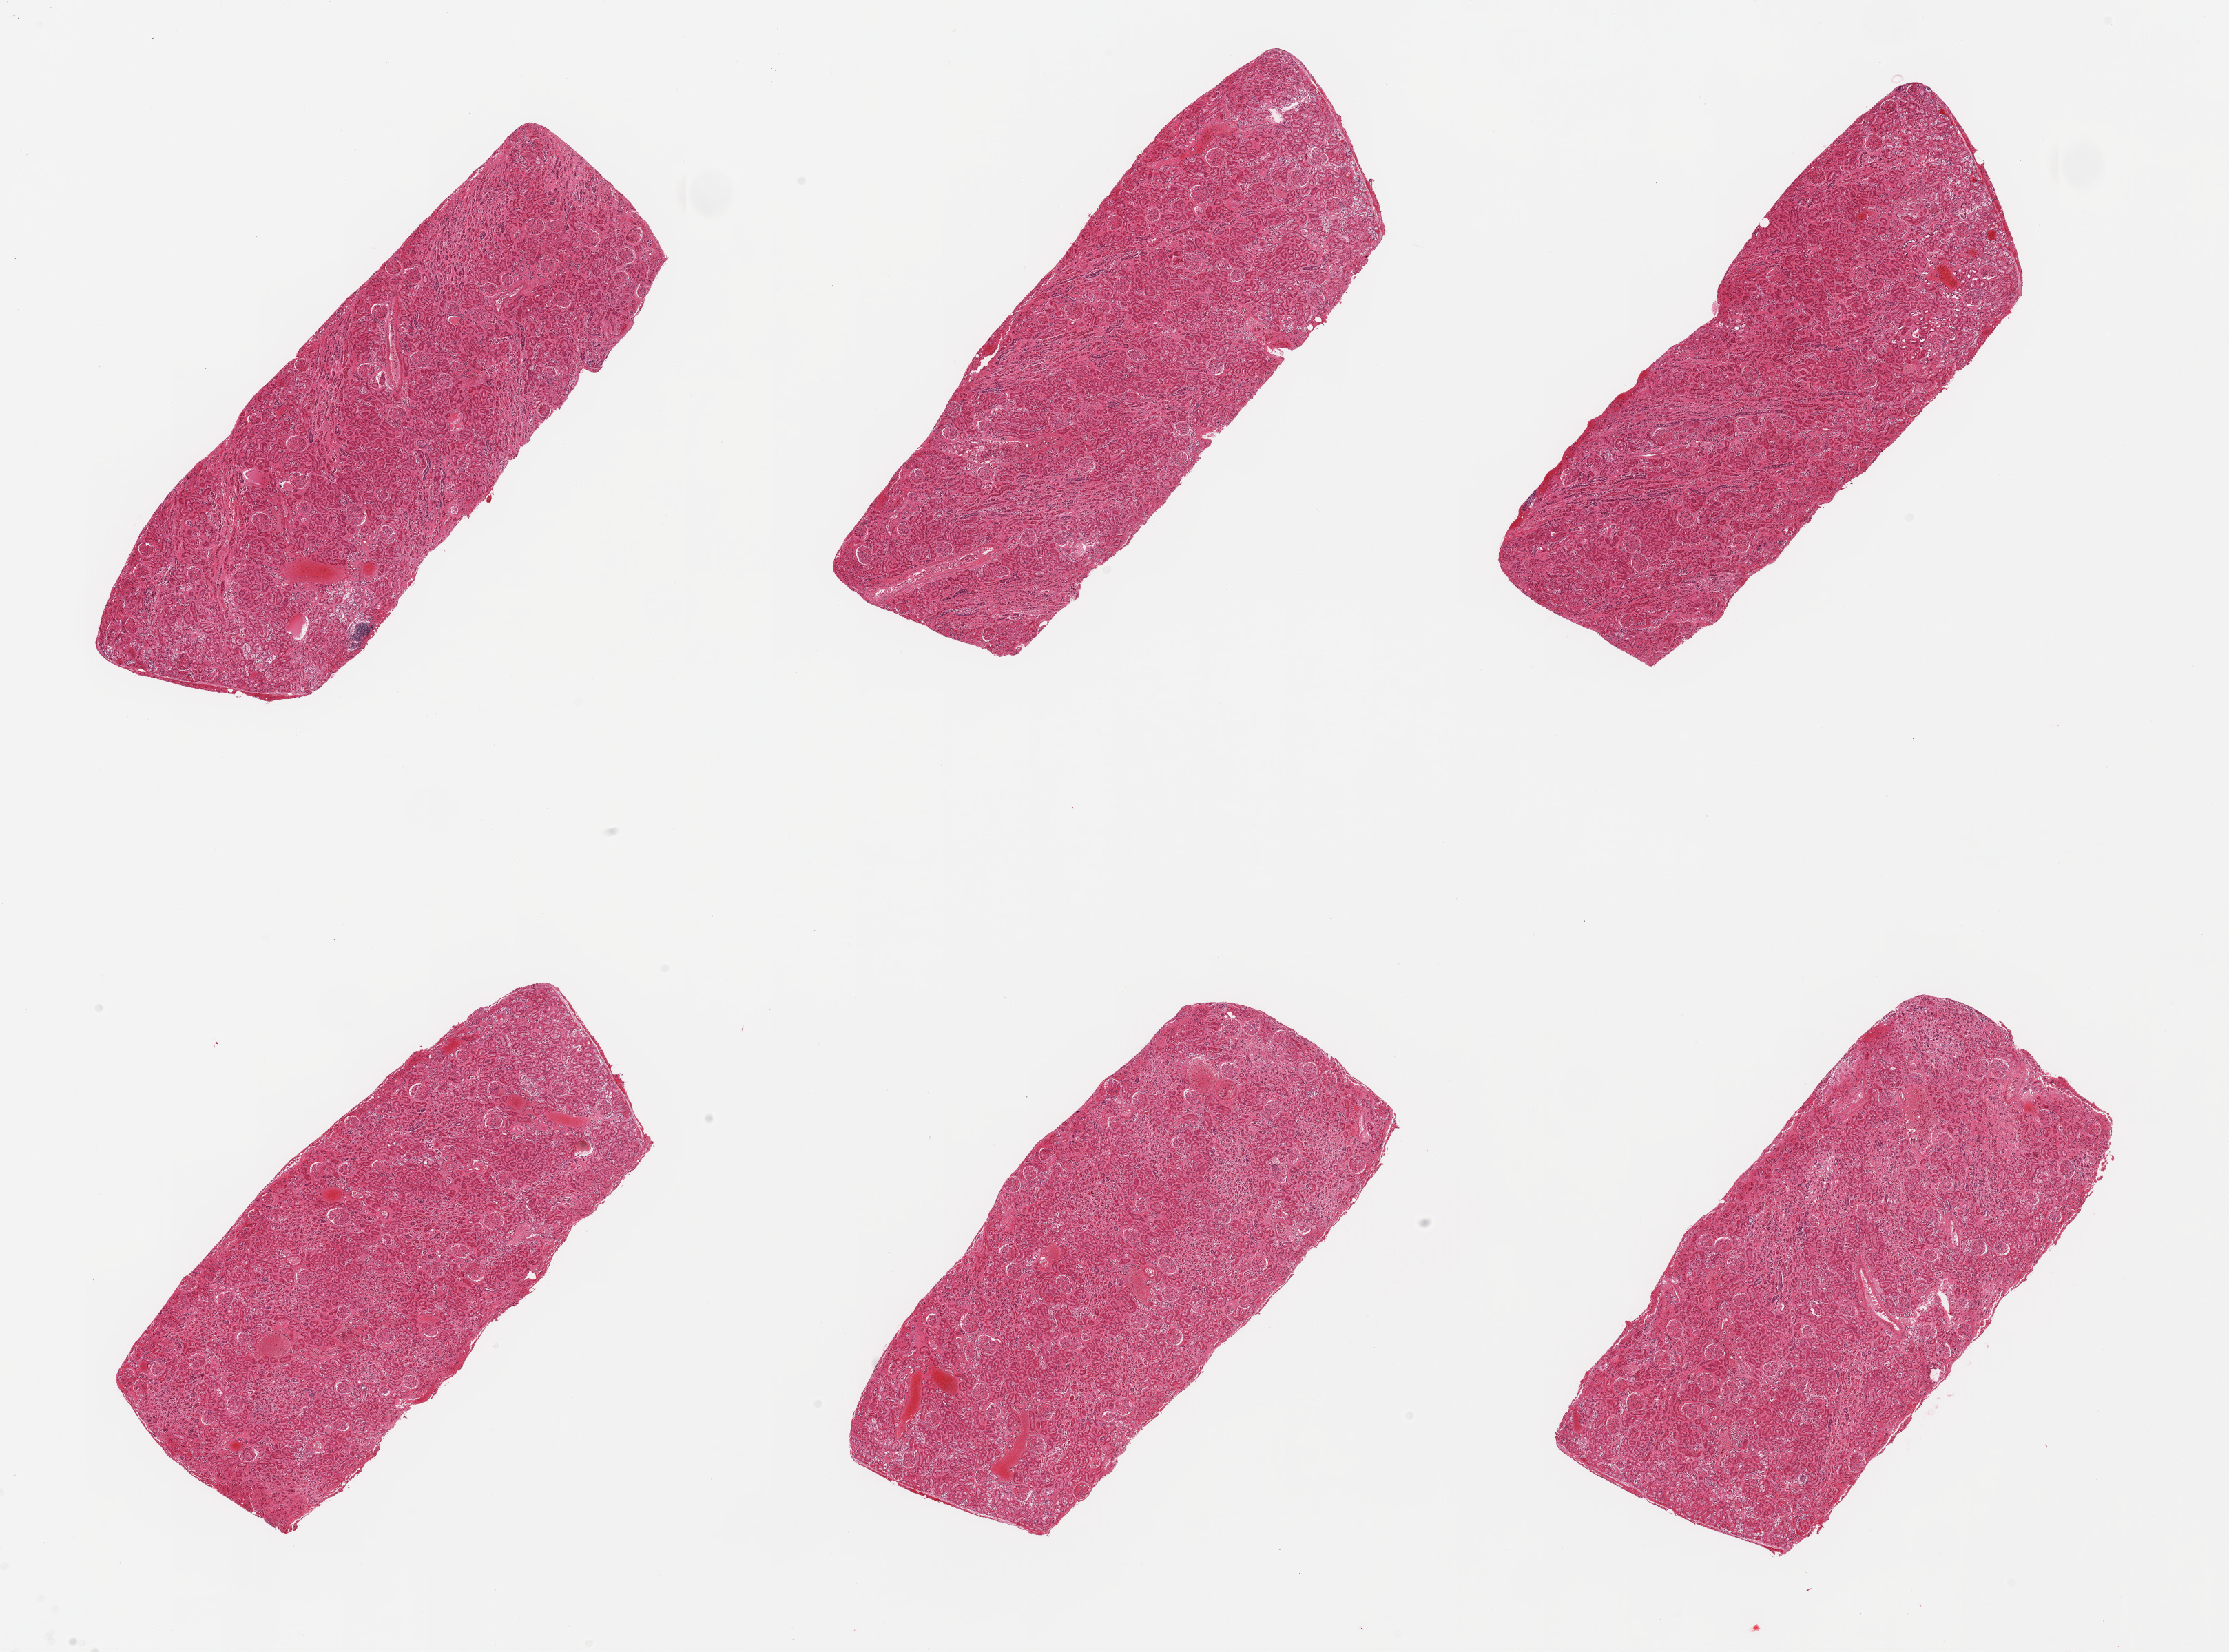
Whole-slide image, H&E stain, shown as a low-resolution overview of the whole scanned area (about 25.6 x 19.0 mm, from a 20x scan), PAXgene-fixed paraffin-embedded (PFPE) section, sampled site (target tissue): renal cortex, donor tissue sample. Donor sex: male.
* pathologist's review note for this sample: 6 pieces;congestion; no chronic or recent lesions